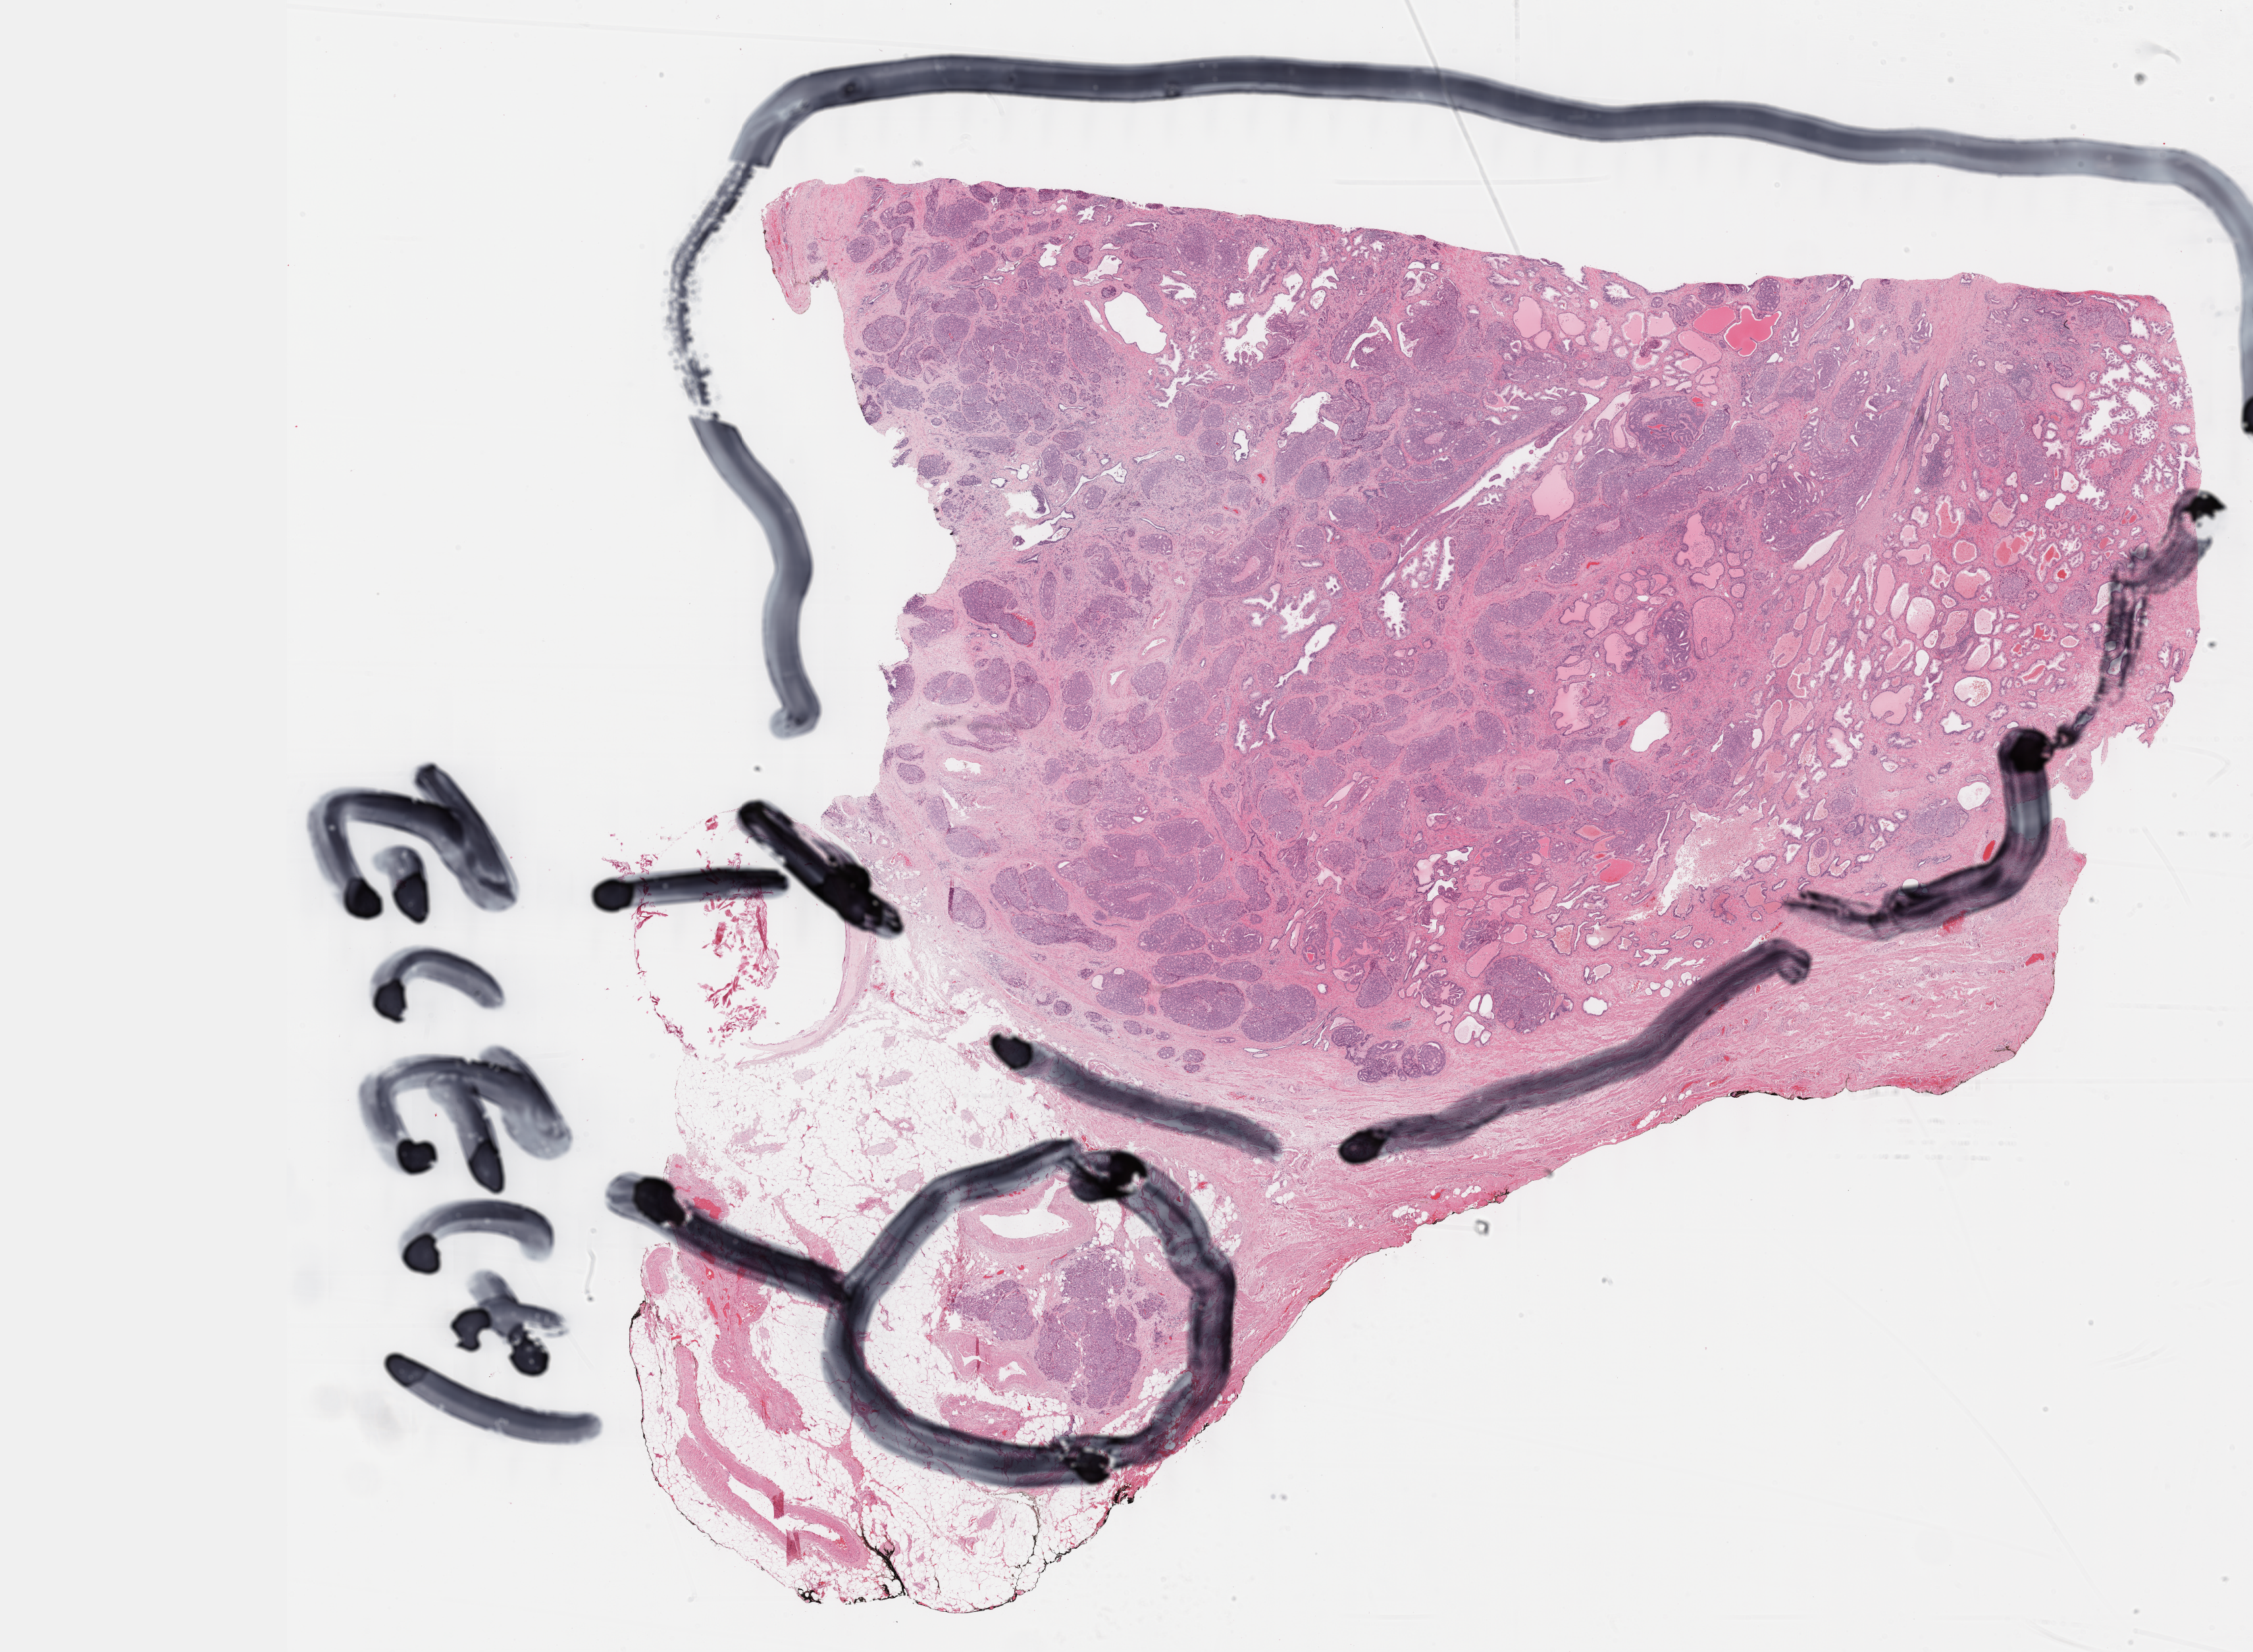
Whole-slide histology image, H&E, low-resolution overview of the scanned area, about 27.2 x 20.0 mm (acquisition: 40x scan), formalin-fixed paraffin-embedded (FFPE) diagnostic section, prostate, primary tumour sample. Male patient; age at initial diagnosis 59 years. Gleason score: 9 (4+5).
- diagnosis: Adenocarcinoma, NOS (prostate gland)
- lymph nodes positive (case pathology): 0 of 15 examined